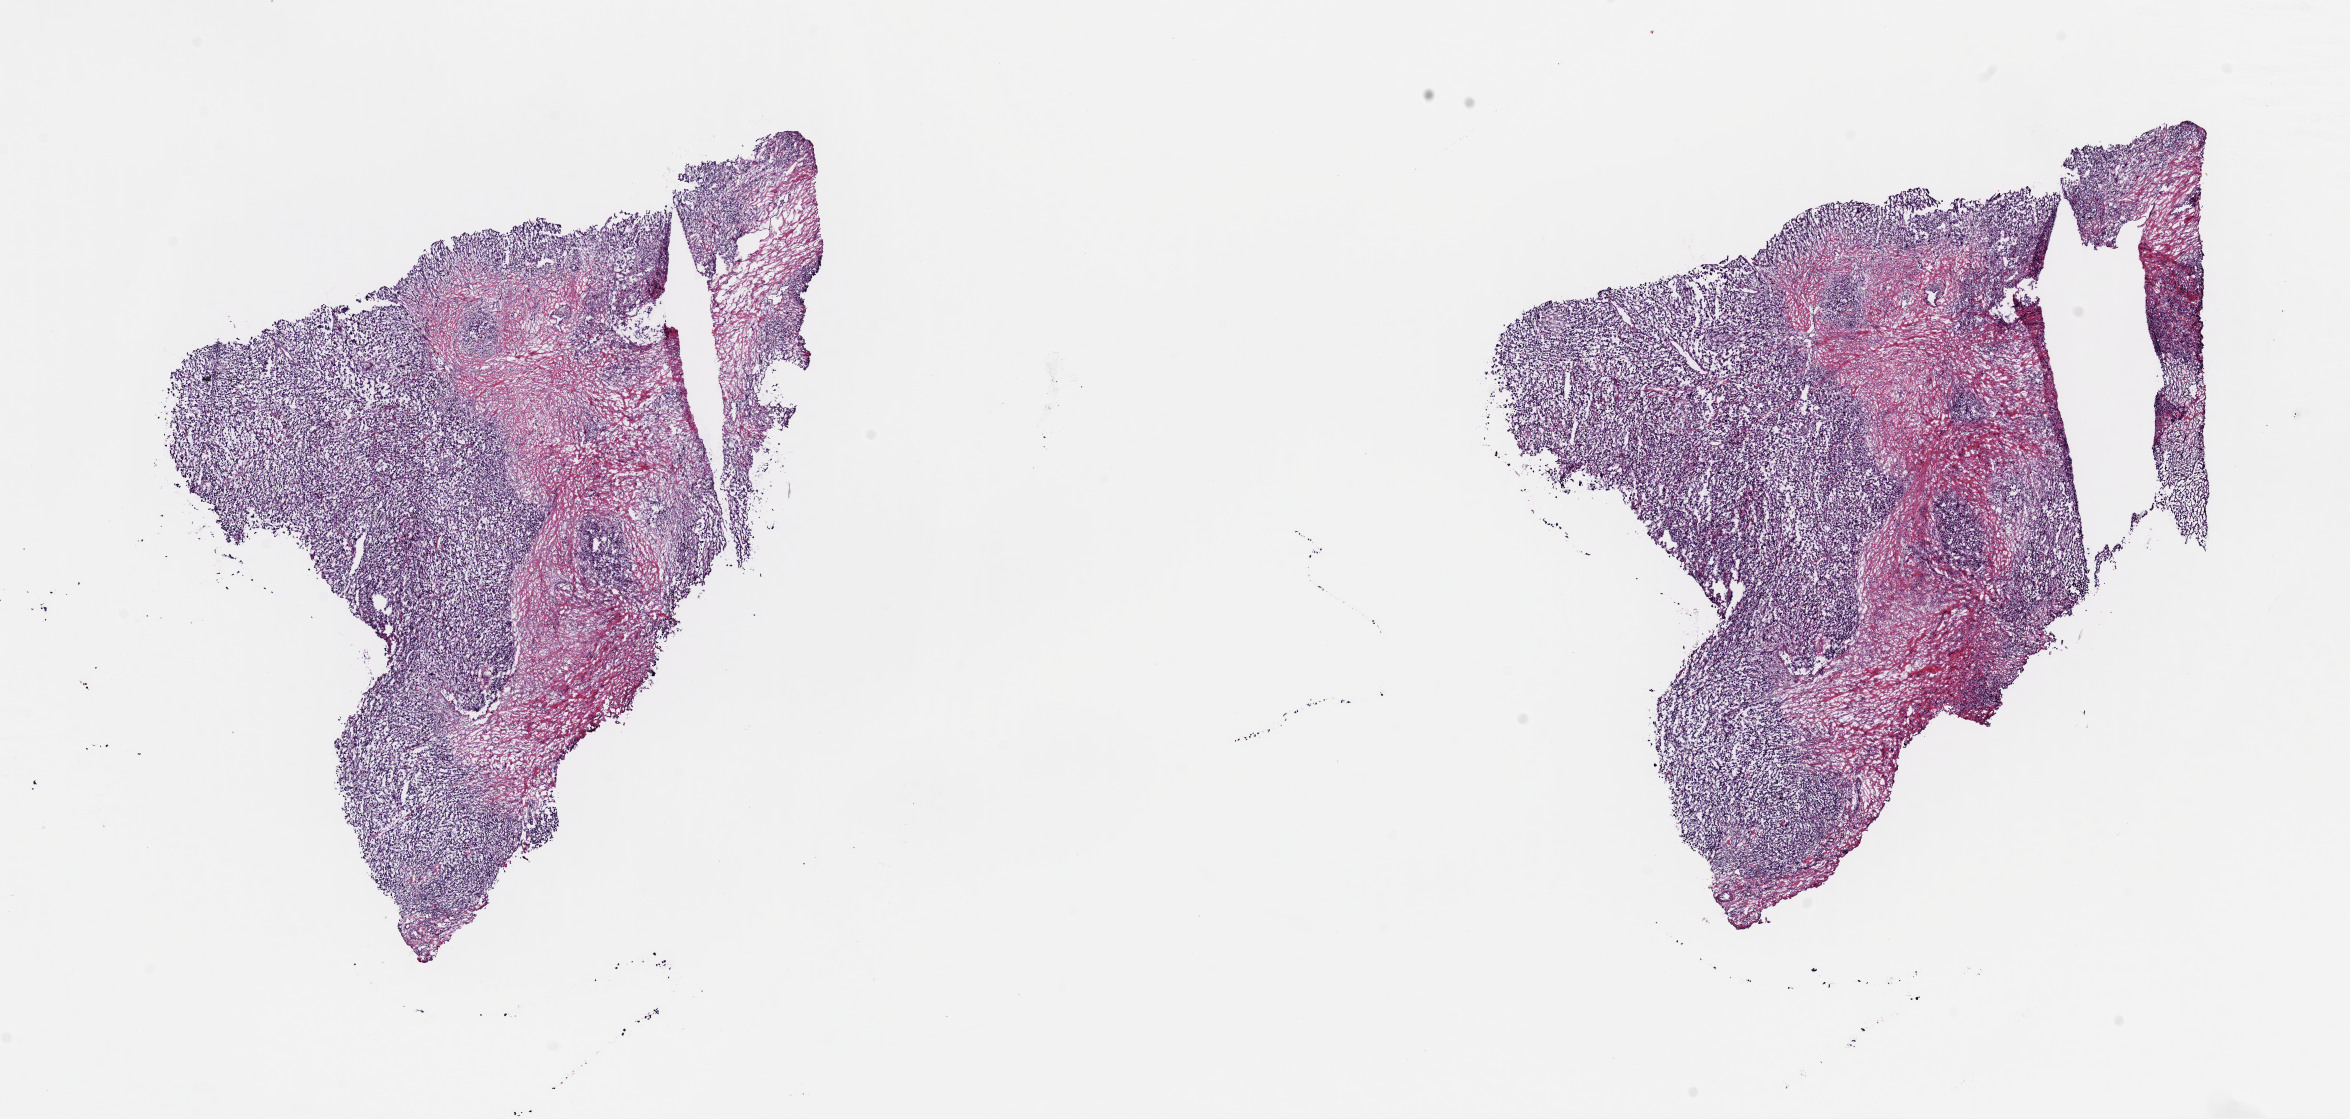
H&E-stained whole-slide image, low-resolution overview of the scanned area, about 18.6 x 8.8 mm; frozen section; metastatic tumour sample, sampled site: lymph node. Patient: male, age at initial diagnosis 74 years. Slide review estimates, as recorded: tumour cells 70%, tumour nuclei 75%, normal cells 0%, stromal cells 30%, necrosis 0%. Infiltration values recorded for this section: lymphocyte infiltration 0%, monocyte infiltration 0%, neutrophil infiltration 0%.
This section: metastatic tumour tissue. Patient diagnosis: Malignant melanoma, NOS.